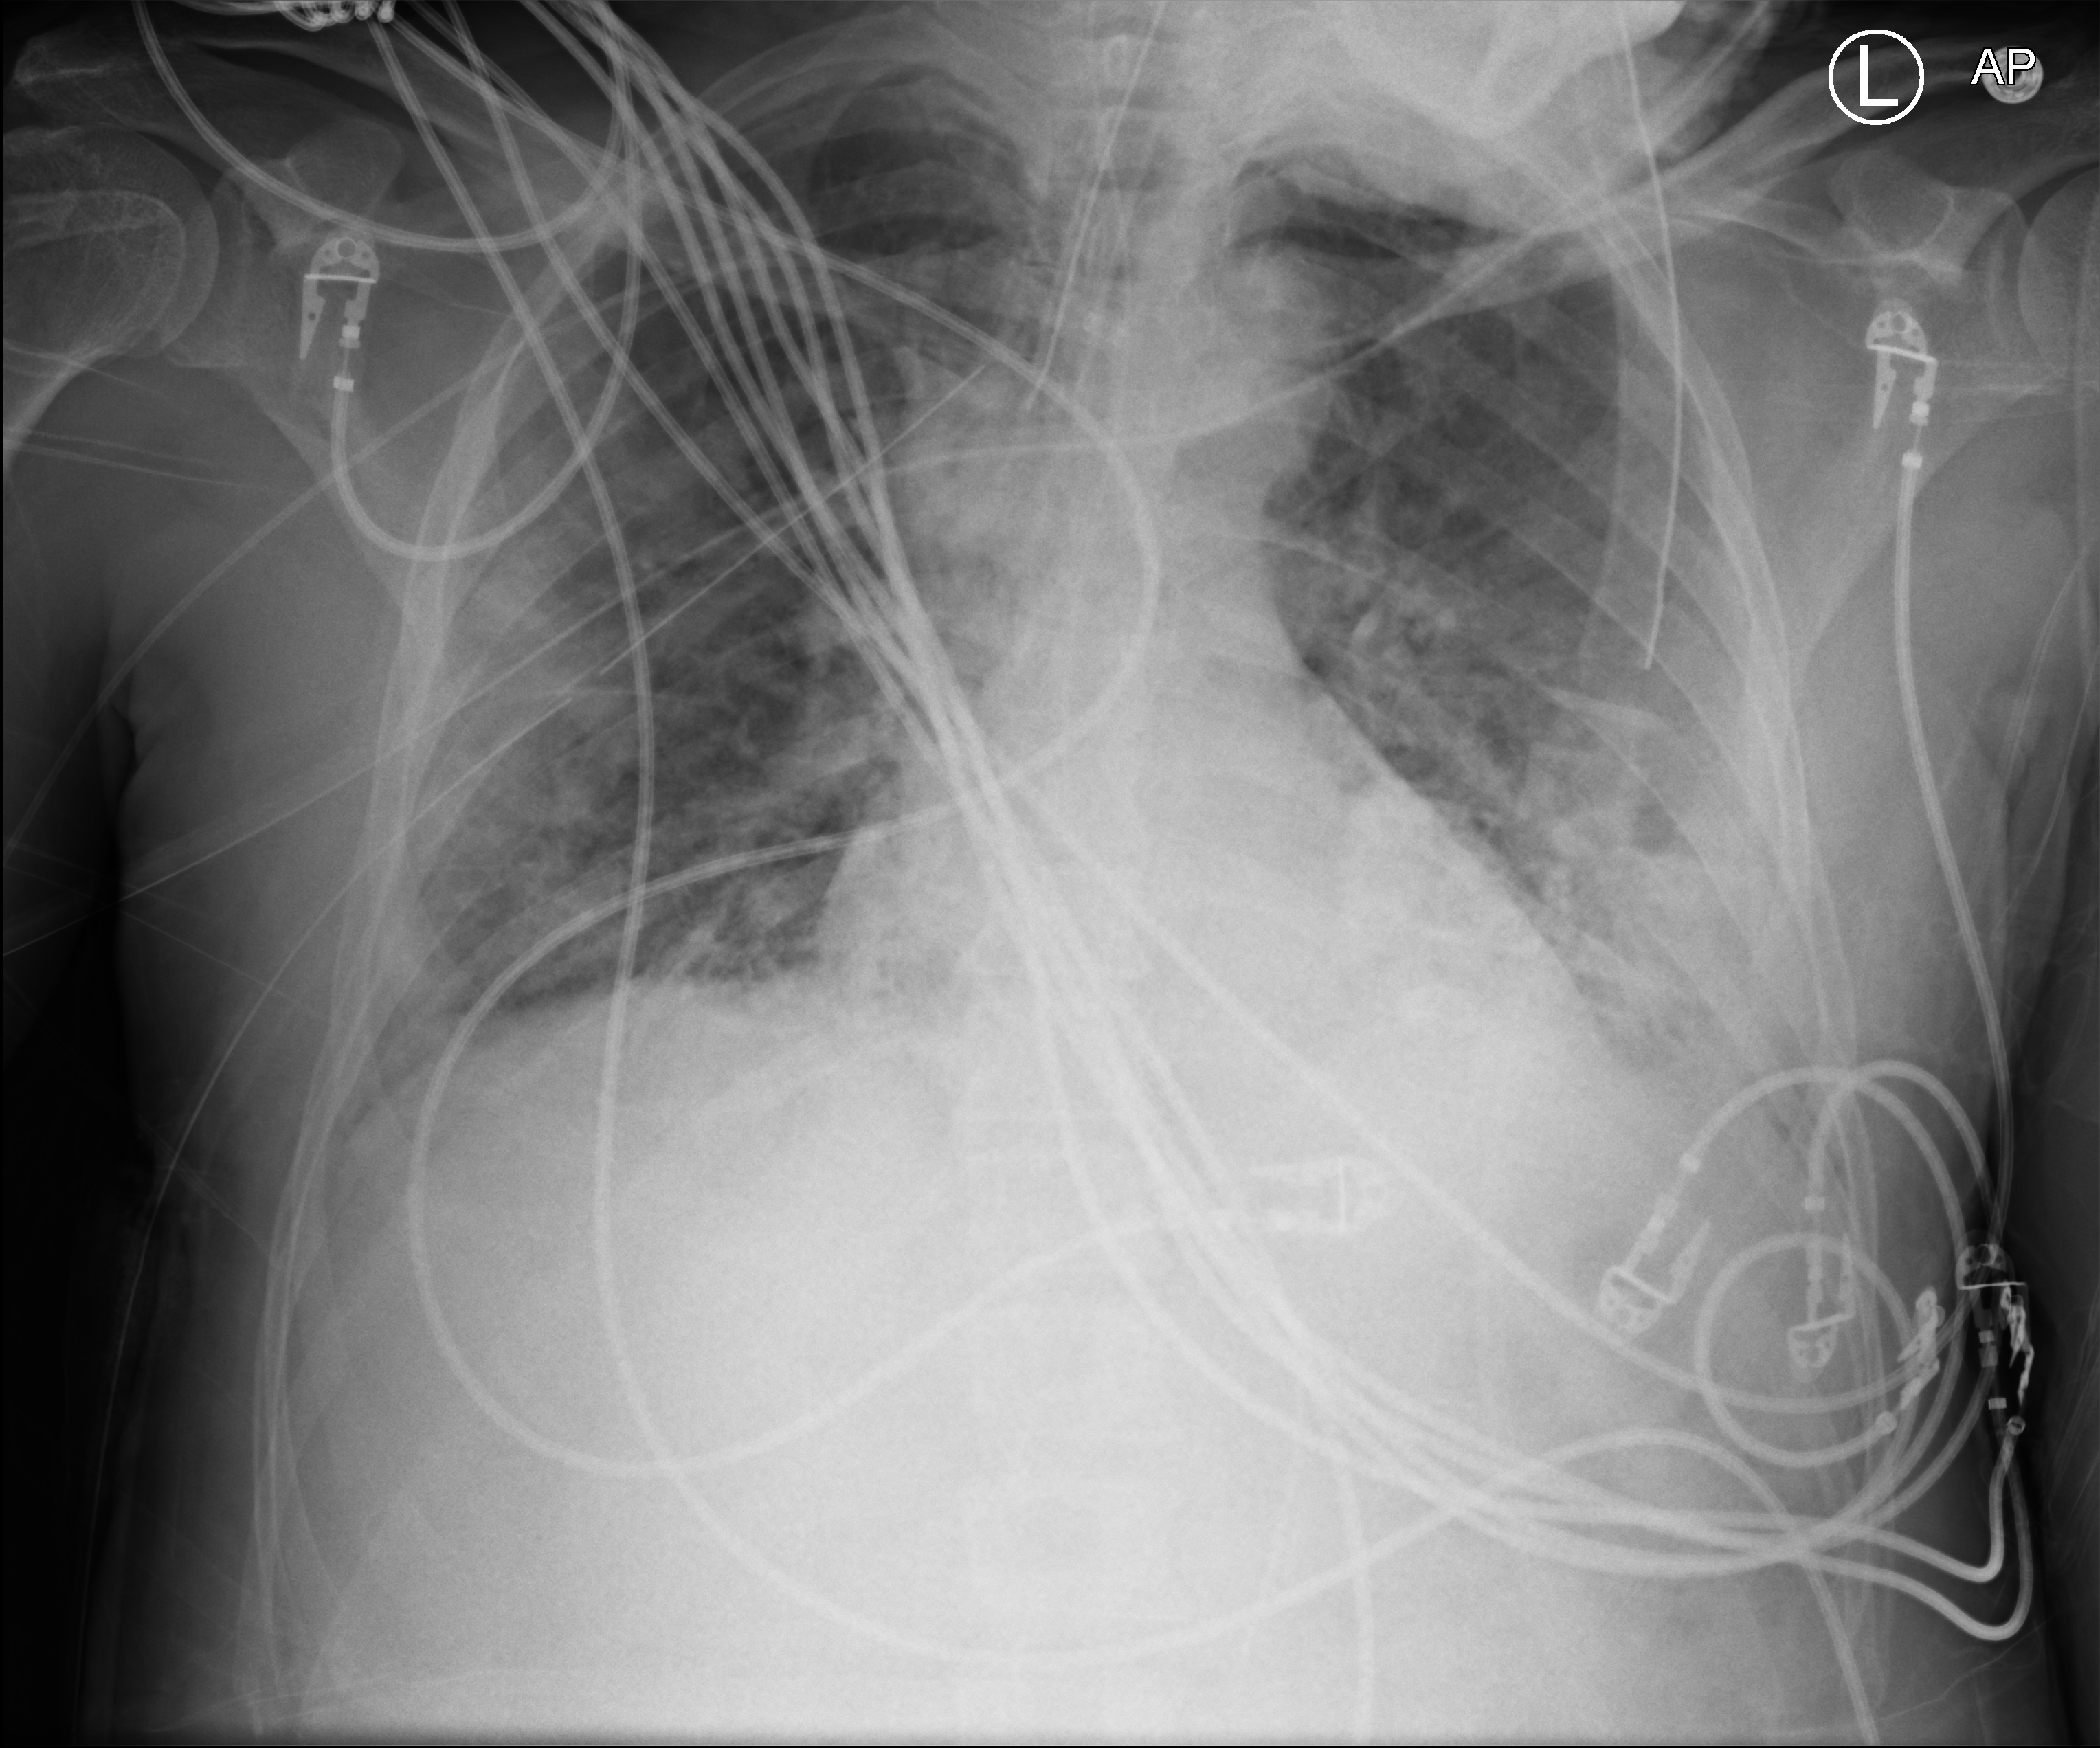
Chest X-ray (portable); anteroposterior (AP) projection. Male patient hospitalised with COVID-19, age 18–59 years.
Admission-level facts for this patient (not findings on this image; timing relative to this image not recorded): length of hospital stay: 41 days; admitted to intensive care during this hospital stay: yes.